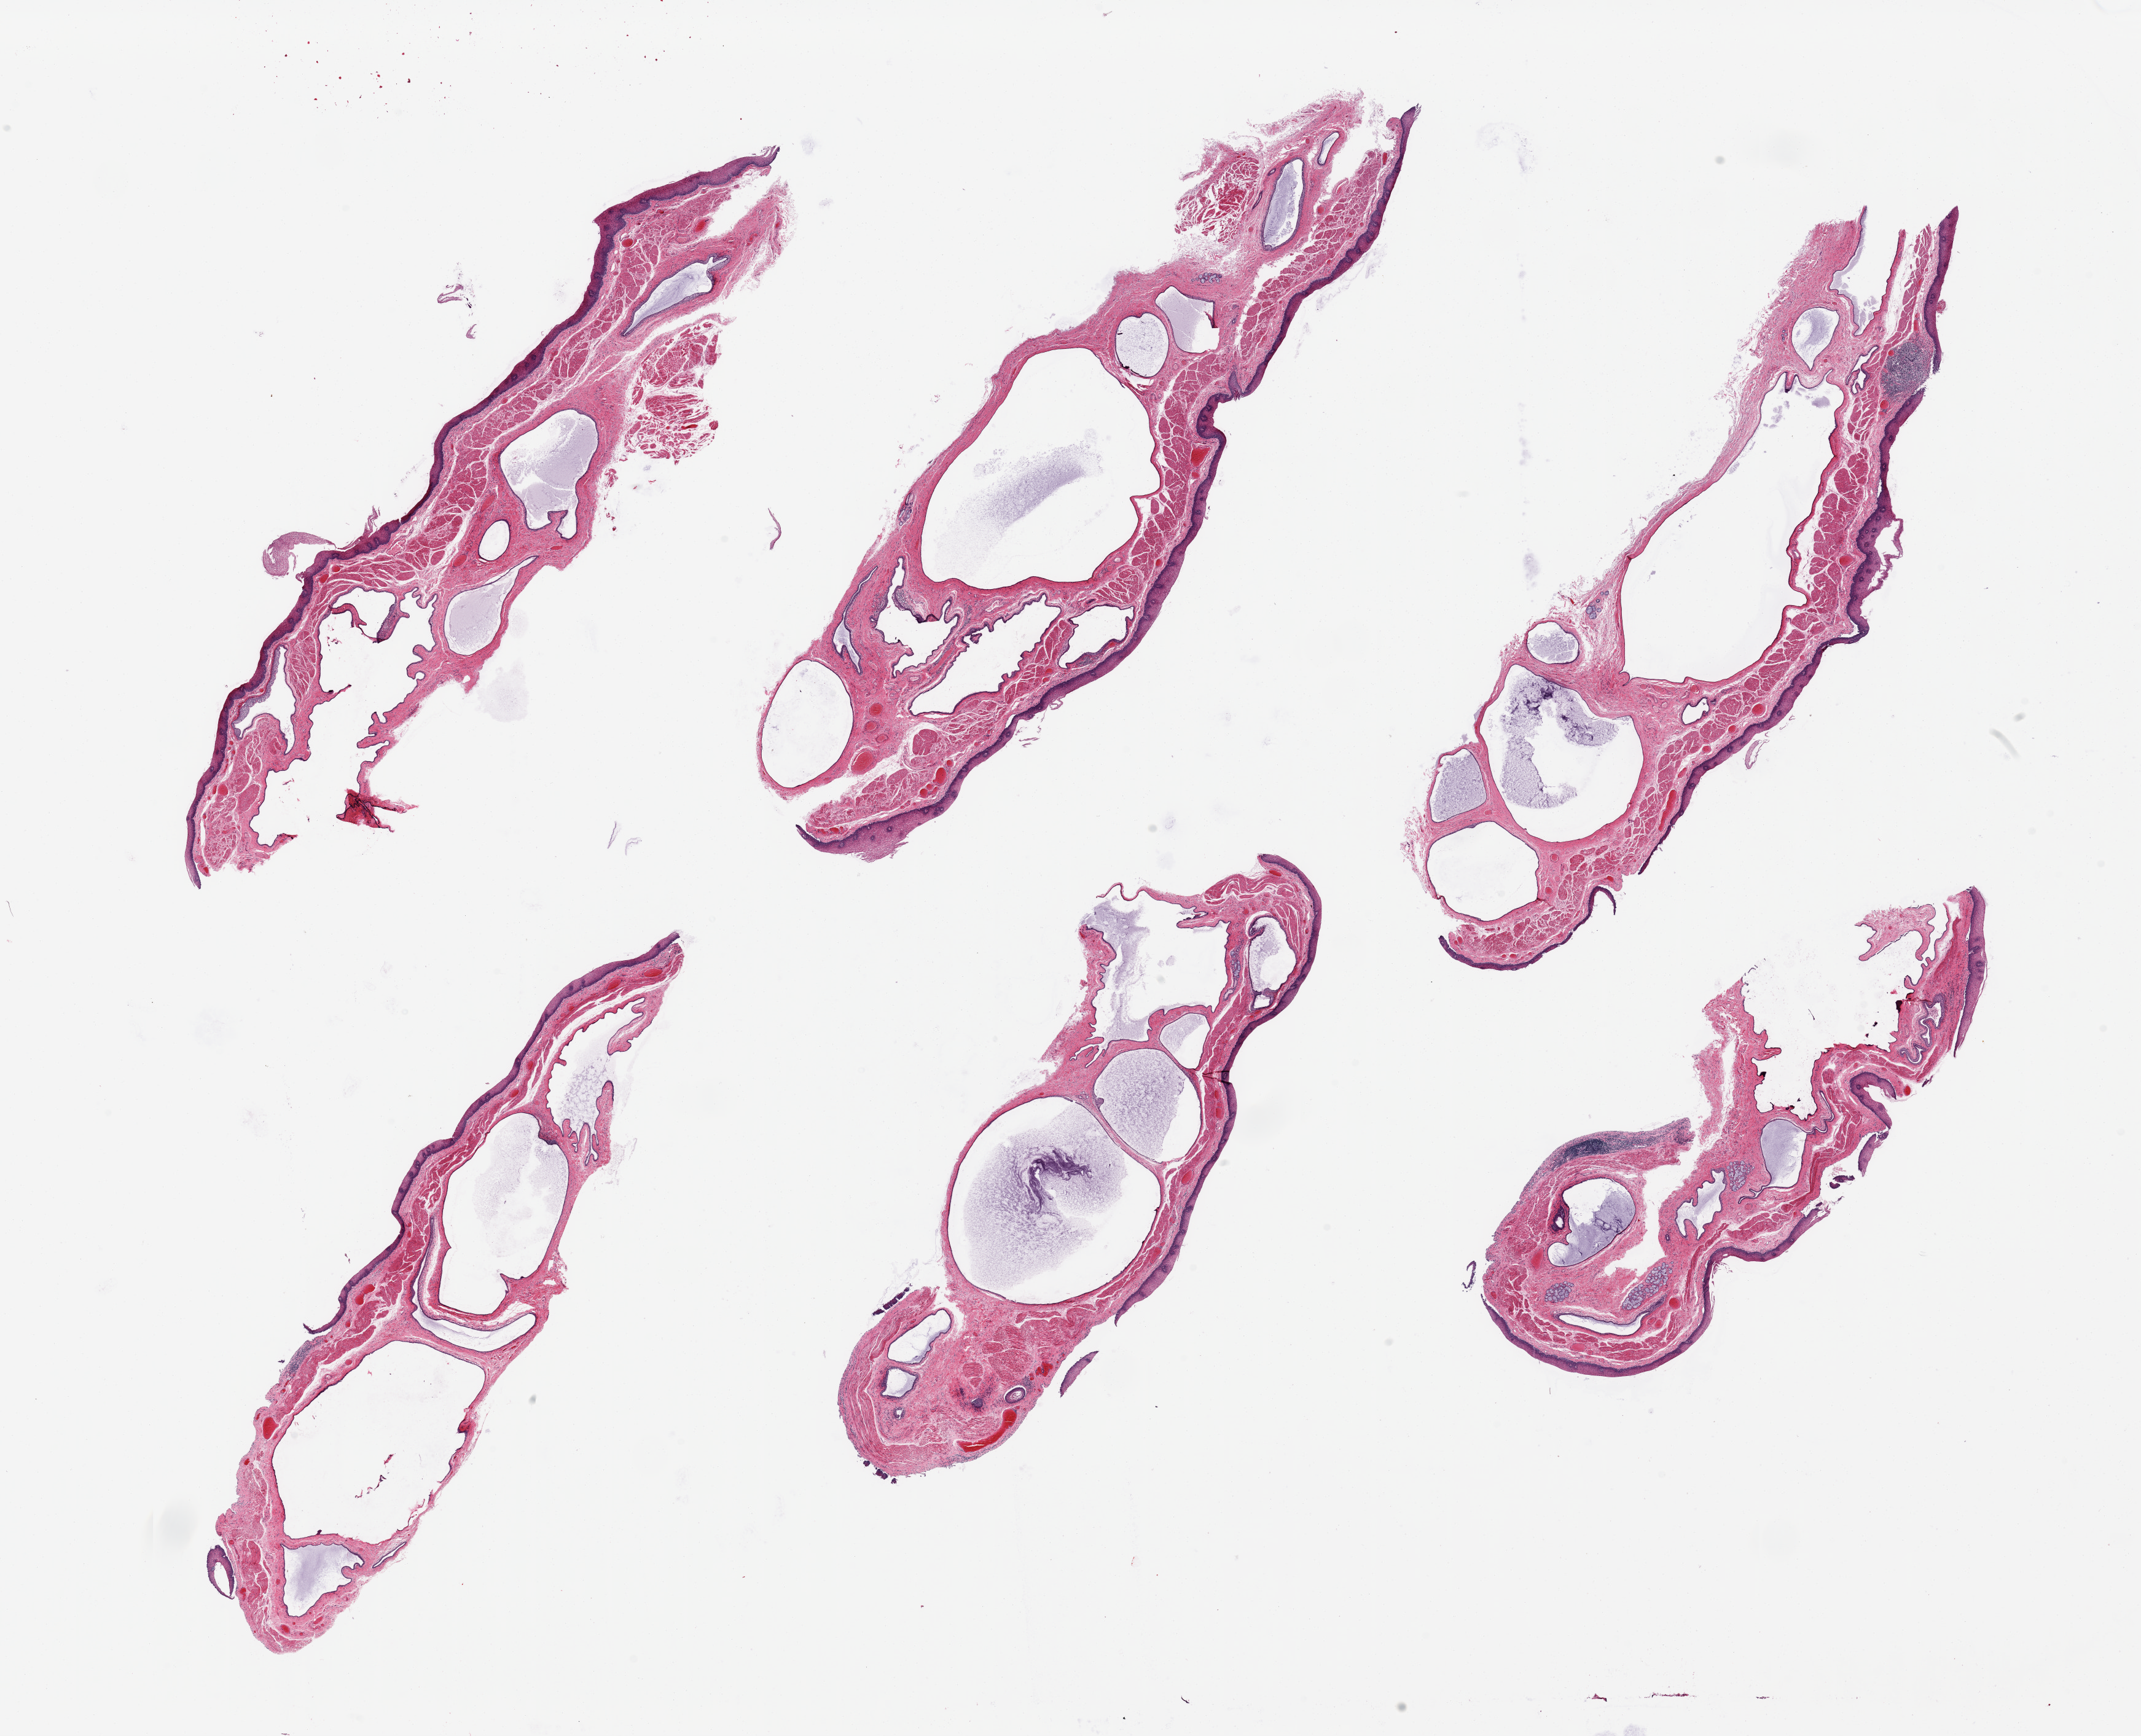
Hematoxylin and eosin (H&E) whole-slide image, whole scanned area (about 27.6 x 22.4 mm) shown as a low-resolution overview, PAXgene-fixed paraffin-embedded (PFPE) section, section of esophageal mucous membrane (target tissue), donor tissue sample. Donor sex: male.
* review note (as recorded): 6 pieces; mucosa well preserved; severe submucosal ductal dilatation with focal lymphoid aggregates